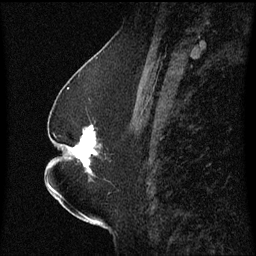
Breast MRI (dynamic contrast-enhanced), one sagittal slice; slice 28 of 60 in the series (ordered by position); dynamic contrast-enhanced series, image 2 of 3 at this slice position (ordered by acquisition); 1.5 T; TE 4.2 ms, TR 8.4 ms; 2.3 mm slice thickness; 256 × 256 image matrix, field of view 200 × 200 mm. Female patient, age 52 years. Case-level facts recorded for this patient, not image findings: setting: breast cancer imaged before/during neoadjuvant chemotherapy; receptor status: HR-positive, HER2-negative.
Outlined on this slice (semi-automatically segmented with operator editing):
- analysis volume of interest (the breast-tissue region the enhancement analysis was run in; not a lesion): bounding box [x1, y1, x2, y2] px = [65, 126, 112, 183]
- tumour enhancement mask (voxels above the 70 % enhancement threshold inside the analysis volume of interest): [74, 126, 98, 173]